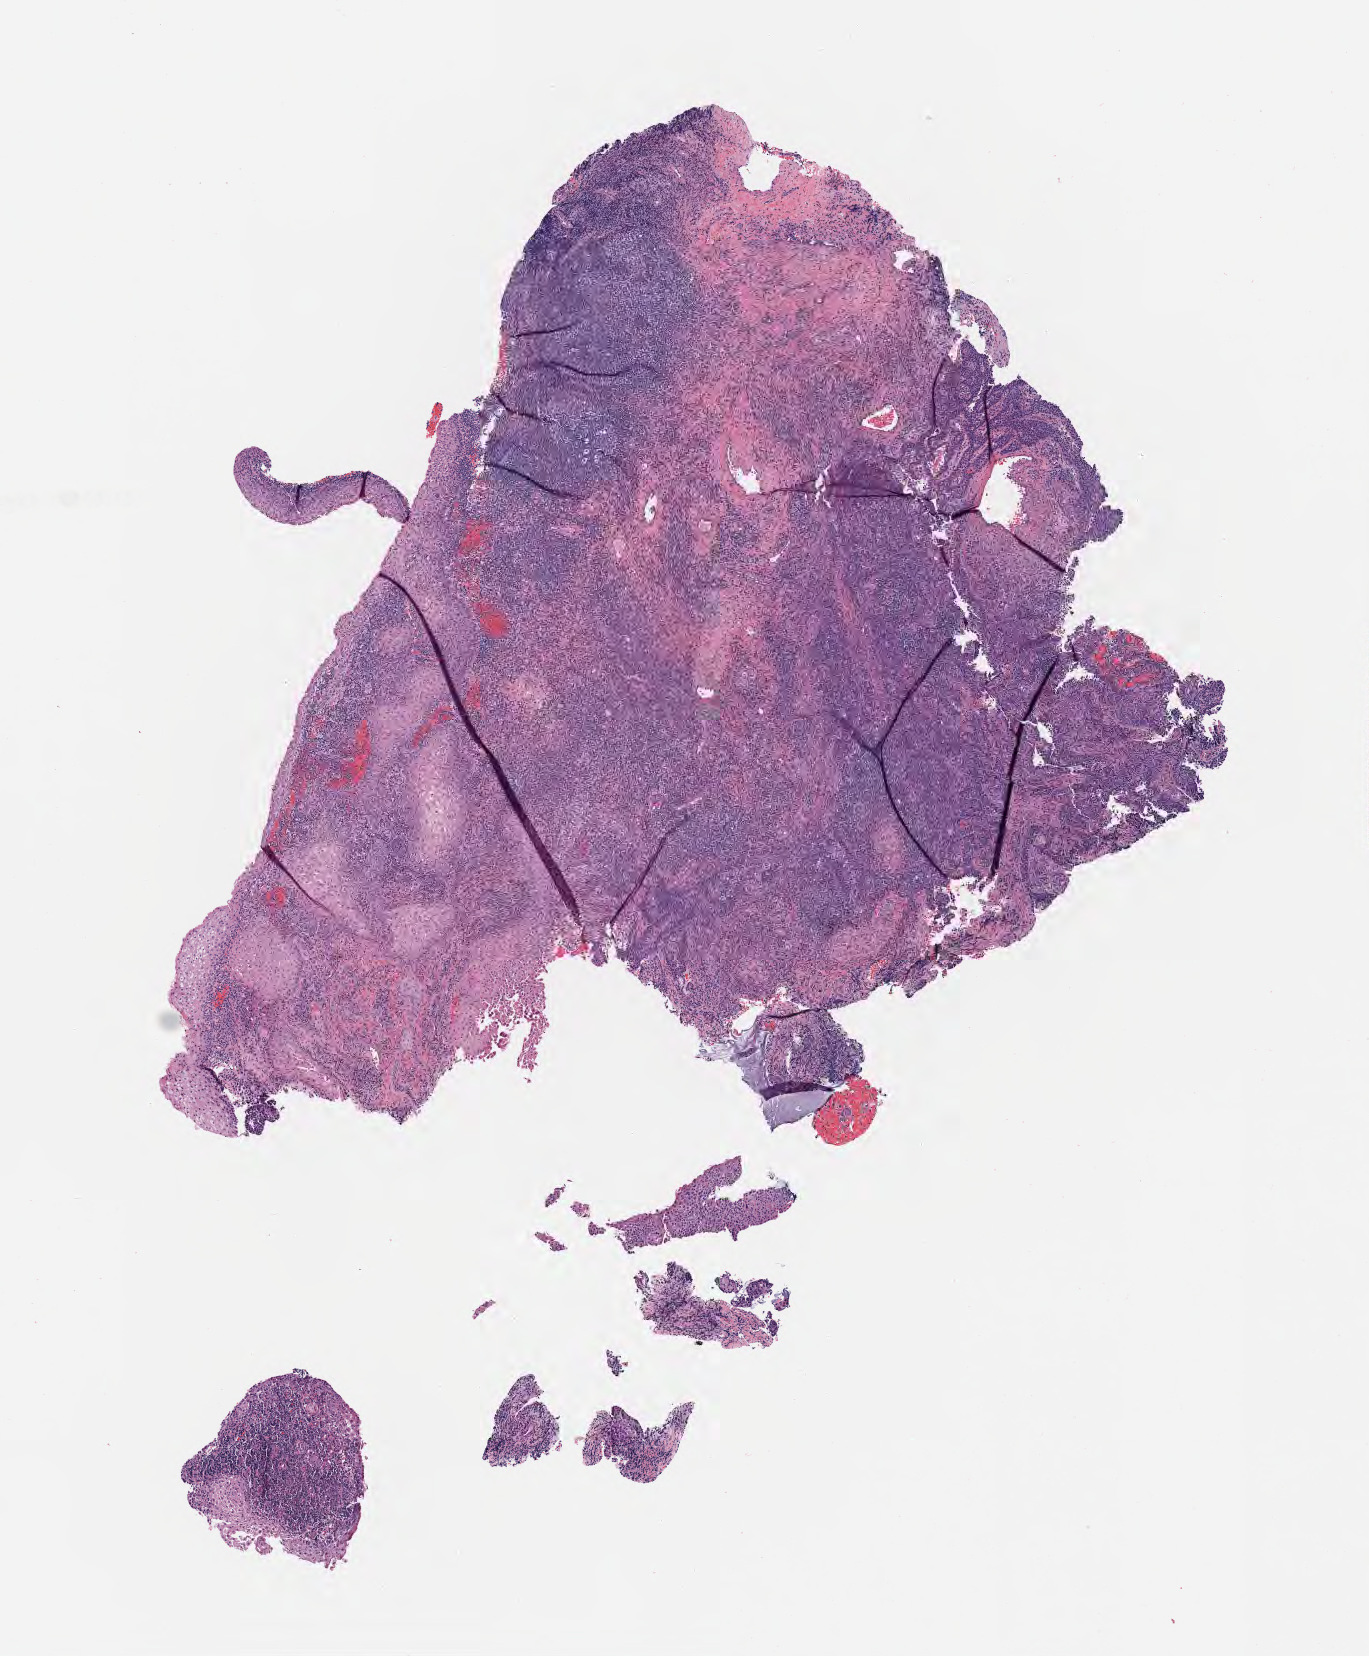
H&E whole-slide image — whole scanned area (about 5.5 x 6.7 mm) shown as a low-resolution overview. Tumor tissue. Site: cervix. Female patient, 36 years old.
Histologic diagnosis: Squamous cell carcinoma, large cell, nonkeratinizing, NOS.